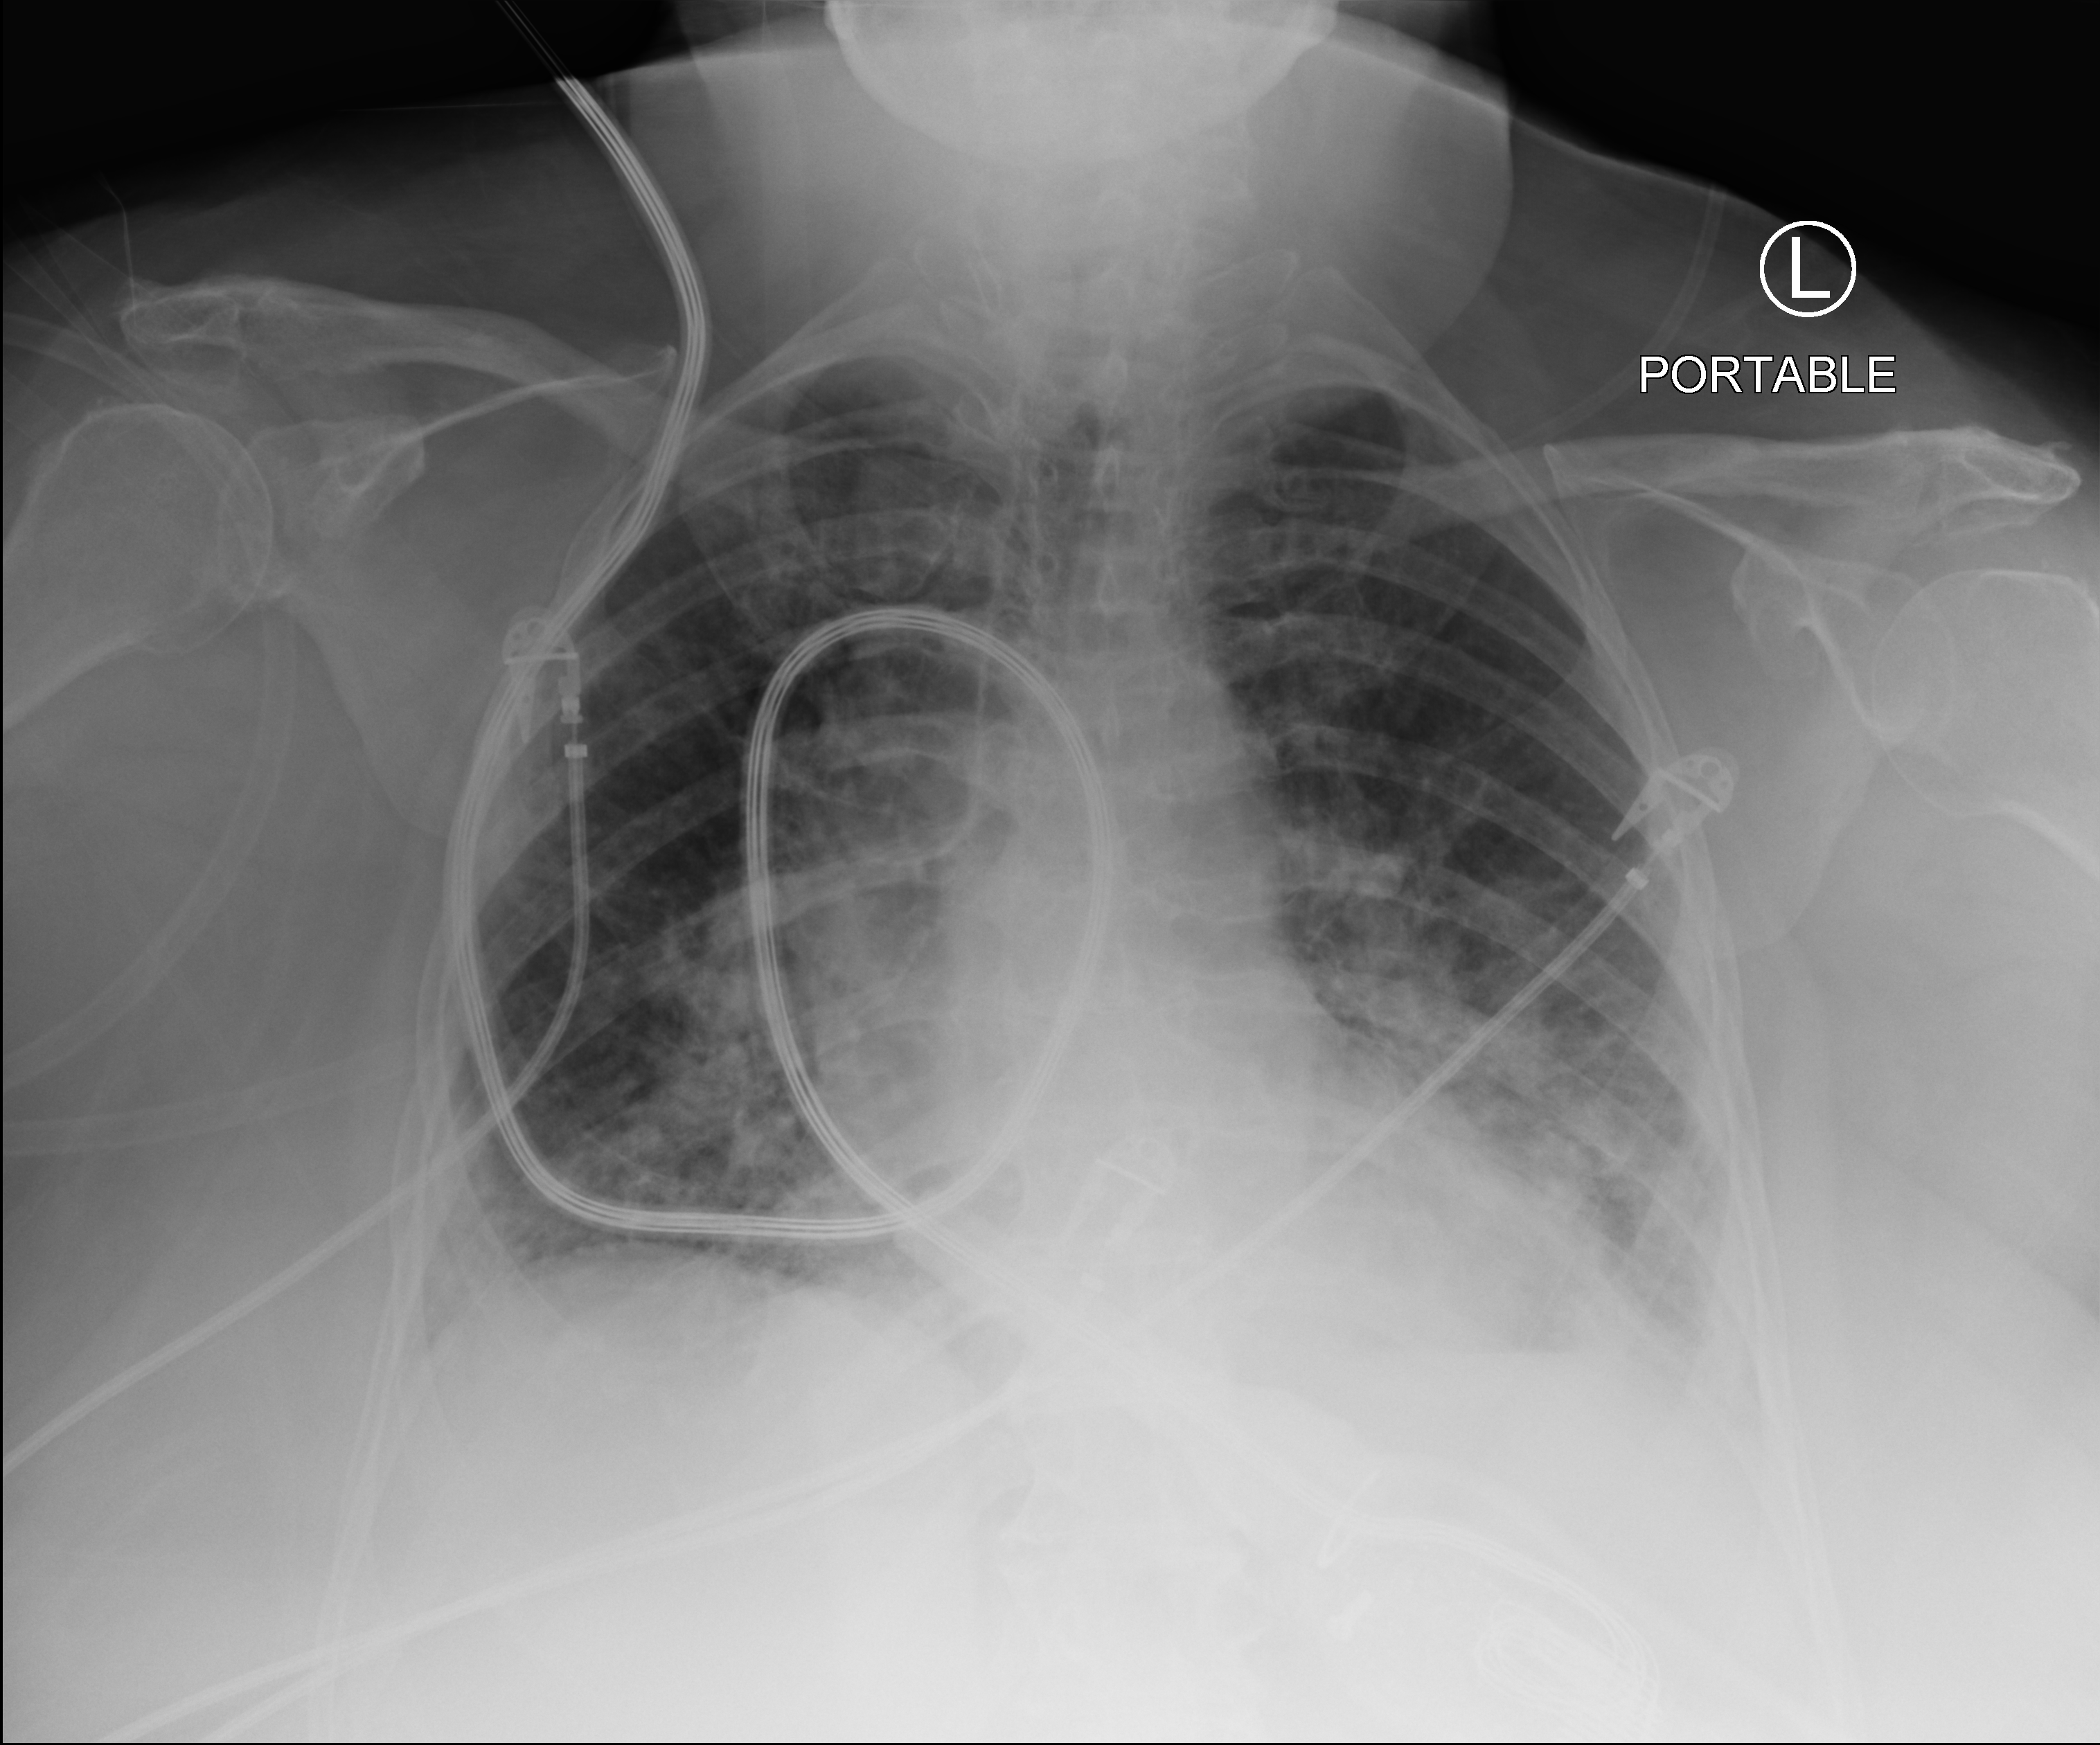
Portable chest radiograph; anteroposterior (AP) projection. Female patient hospitalised with COVID-19, age 75–90 years.
Admission-level facts for this patient (not findings on this image; timing relative to this image not recorded): mechanically ventilated during this hospital stay: no.